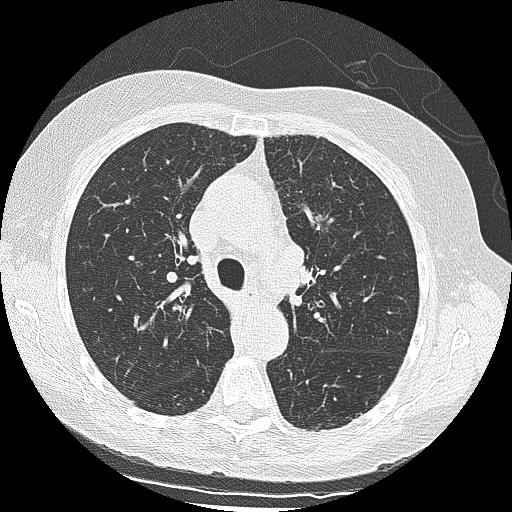
Low-dose screening chest CT, one axial slice; slice 97 of 139 in the series (ordered by position); lung window (W 1500 / L -600 HU); 2.5 mm slice thickness; 512 × 512 image matrix.
Structures marked on this image (manually delineated by an expert):
- lesion 1 (tumor, upper lobe of left lung): bounding box [x1, y1, x2, y2] px = [313, 214, 334, 226]